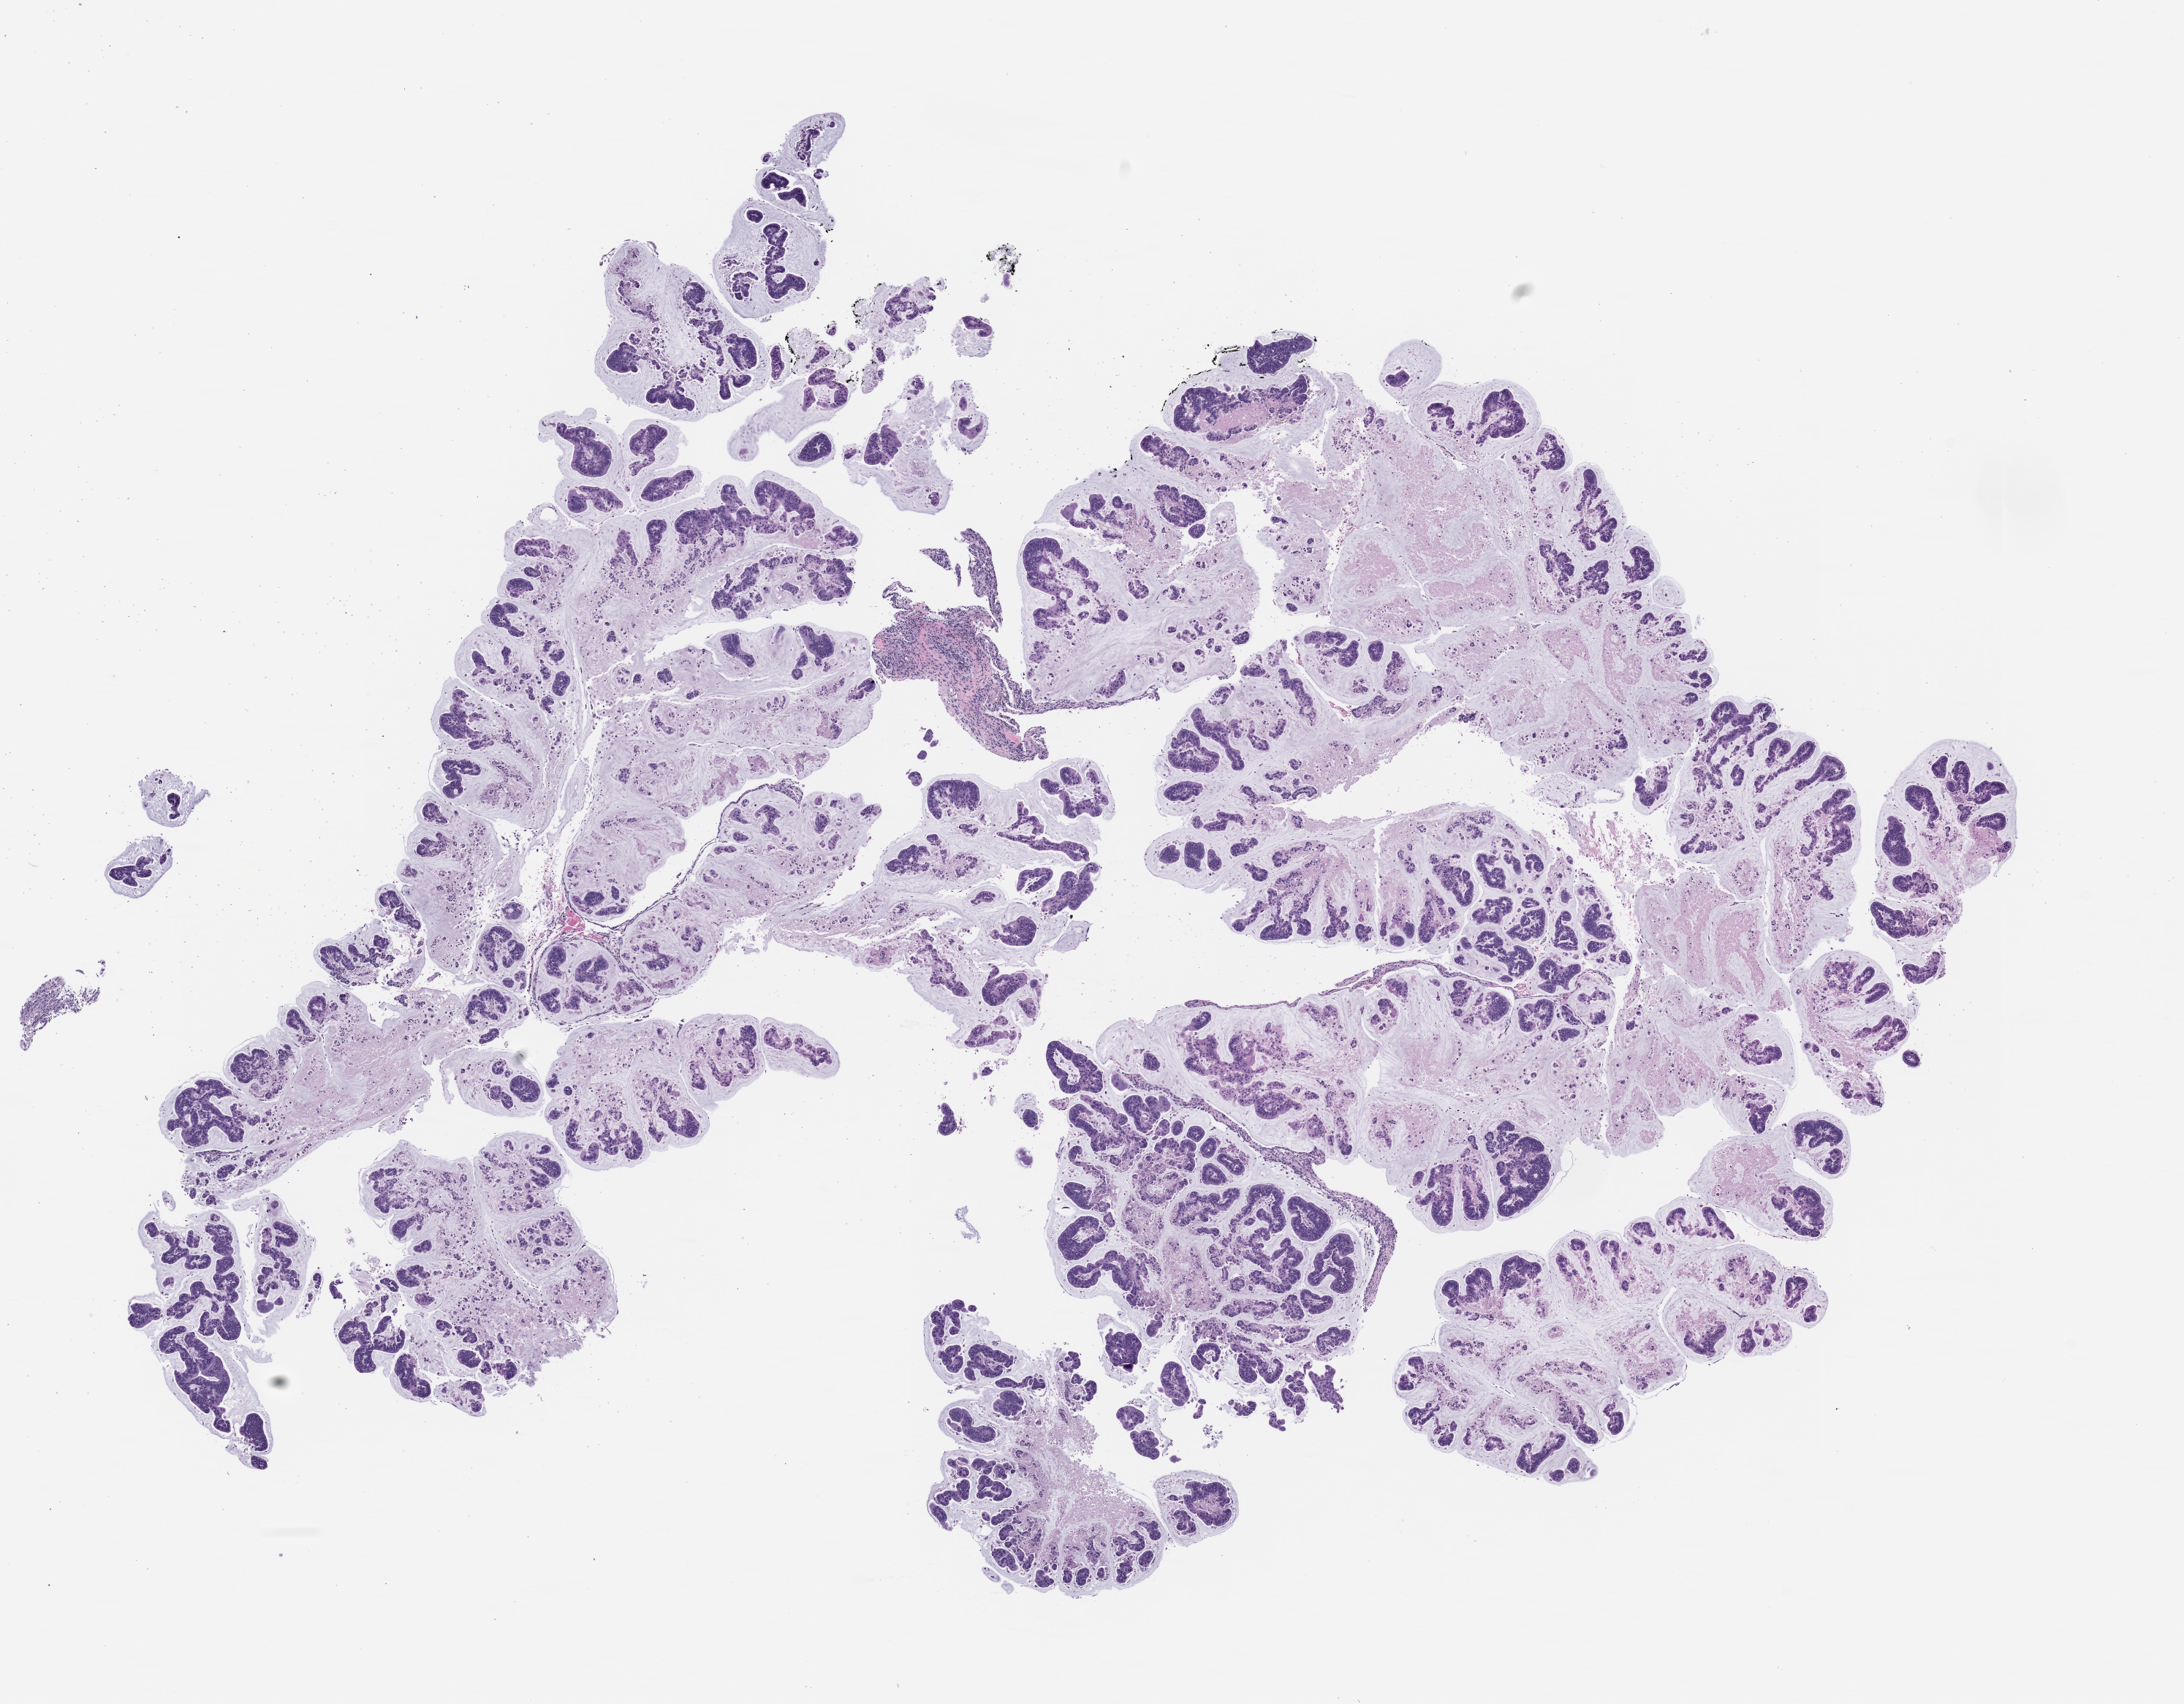
Whole-slide image, H&E: patient-derived xenograft (human tumor grown in a mouse), passage 0, a low-resolution overview of the entire scanned area, about 12.0 x 9.4 mm, formalin-fixed paraffin-embedded section, originating tumor site category: colon.
• originating patient diagnosis: Colon Adenocarcinoma